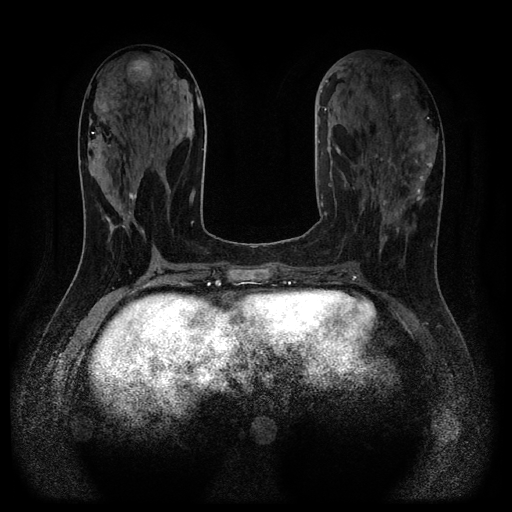
Breast MRI (dynamic contrast-enhanced, multi-phase), one axial slice. Position 45 of 116 along the scan axis. Dynamic contrast-enhanced series, time point 2 of 5 at this slice position (early post-contrast). 1.5 T. TE 2.7 ms, TR 5.4 ms. 2.2 mm slice thickness. 512 × 512 image matrix. Female patient, age 43 years.
Outlined on this slice (semi-automatically segmented with operator editing):
- breast lesion (labelled benign in the annotation): bounding box (x1, y1, x2, y2) in pixels: (127, 57, 152, 83)